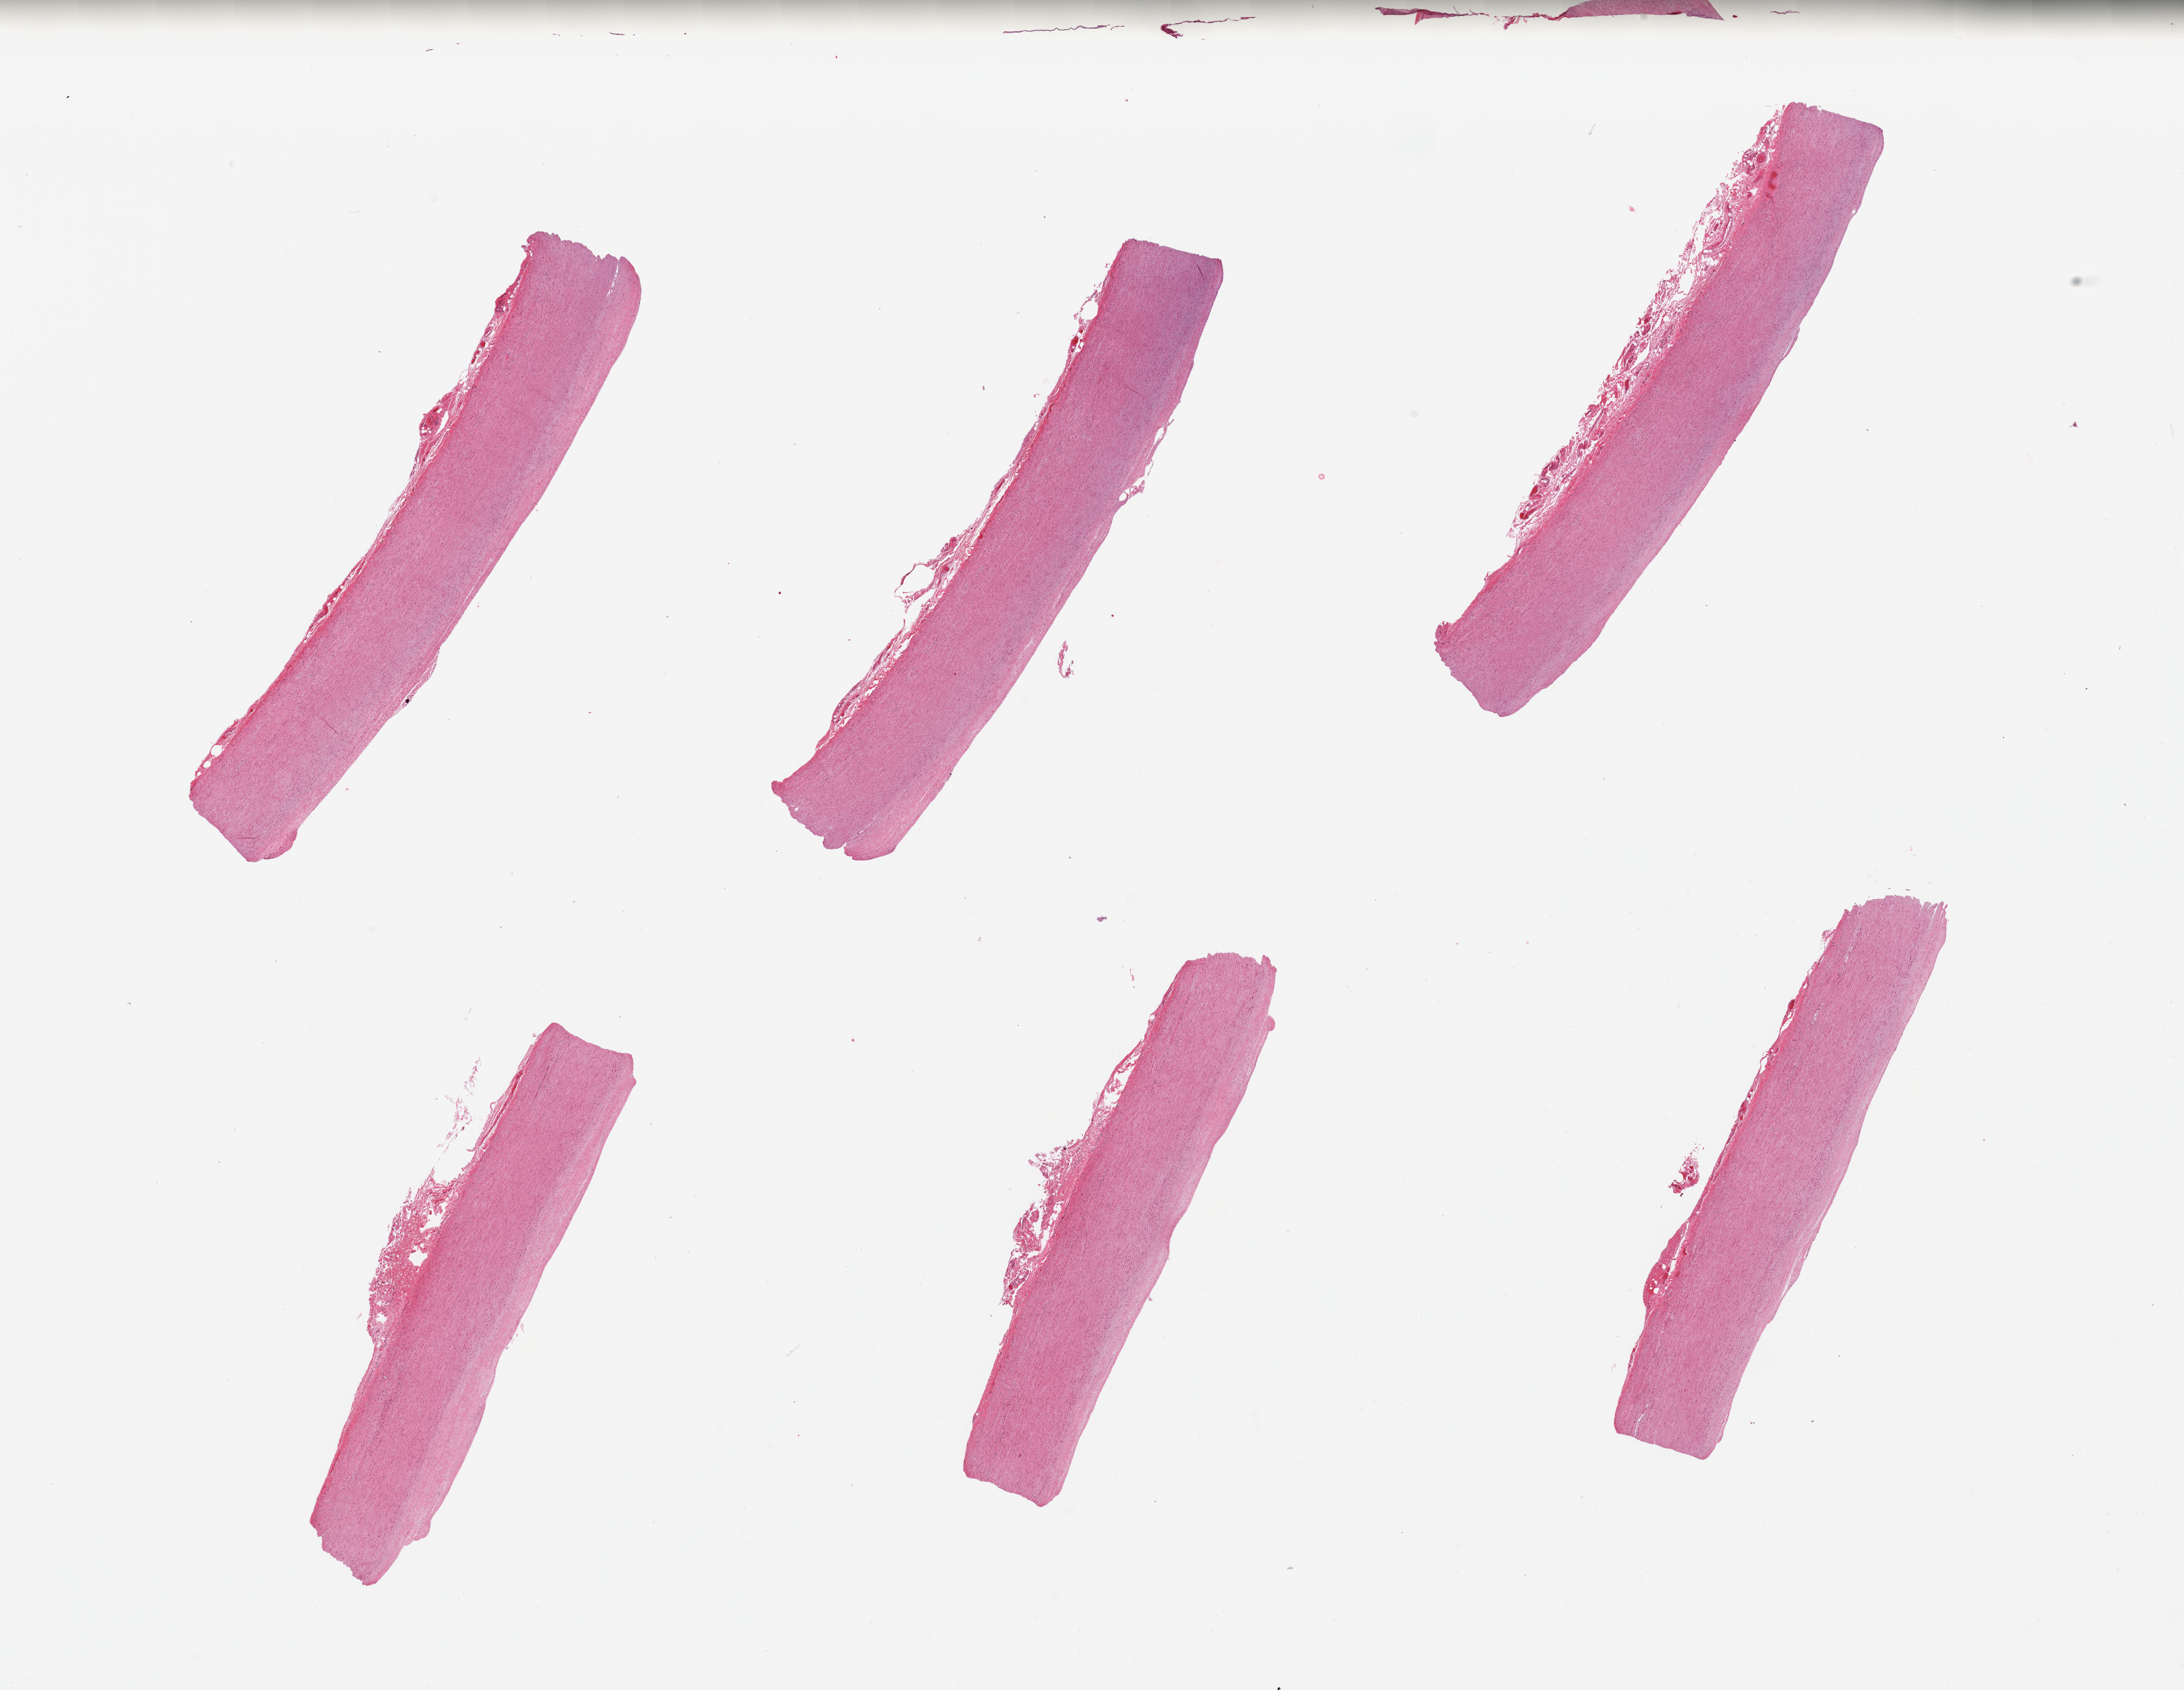
Whole-slide image, H&E stain — shown as a low-resolution overview of the whole scanned area (about 27.6 x 21.3 mm). PAXgene-fixed, paraffin-embedded tissue. Sampled site (target tissue): aorta. Tissue donor sample.
Review note (as recorded): 6 pieces; 3 have thin fibrous intimal plaques.